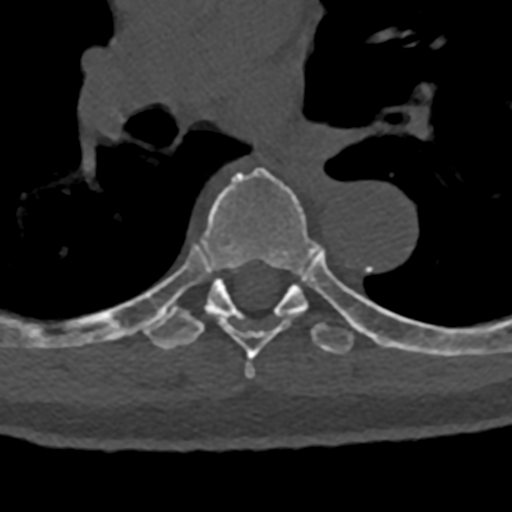
CT including the spine, one axial slice; position 790 of 797 along the scan axis; reconstruction kernel Br40s/3; bone window (W 1800 / L 400 HU); 512 × 512 image matrix, field of view 160 × 160 mm. Patient: male, 74 years. Case-level facts recorded for this patient, not image findings: primary cancer: renal.
Structures marked on this image (semi-automatically segmented with operator editing):
- T6 vertebra: bounding box <148,167,318,379> (left, top, right, bottom; pixels)
- T7 vertebra: <70,245,432,355>